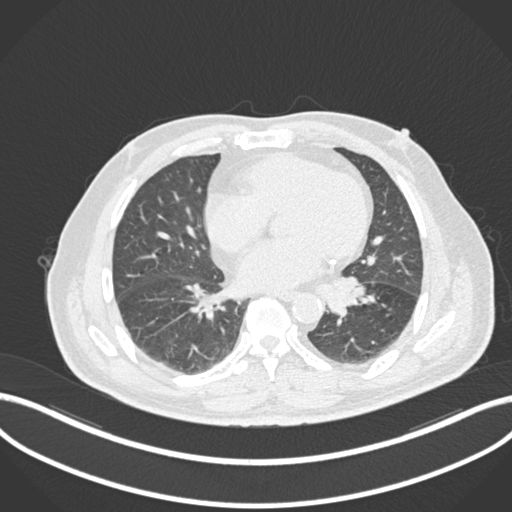
Chest CT, one axial slice. Slice 51 of 161 in the series (ordered by position). Reconstruction kernel B30f. 120 kVp. Lung window (W 1500 / L -600 HU). 1 mm slice thickness. 512 × 512 image matrix, field of view 400 × 400 mm. Male patient, age 71 years. From the clinical record (not read from this slice): clinical TNM (as recorded): T1b N0 M0.
Structures marked on this image (rectangle marked by the reading radiologist):
- lung tumour (recorded histology: squamous cell carcinoma): box from (x=325, y=273) to (x=367, y=320) px